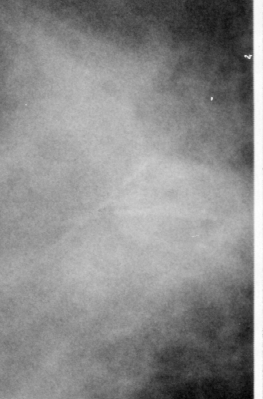
Crop from a digitized film mammogram around one marked abnormality; right breast; CC view; BI-RADS breast density category 3 (scale 1–4).
- Marked abnormality: mass, shape irregular, margins obscured / ill defined; BI-RADS assessment category 4; subtlety rating 3 on a 1 (subtle) to 5 (obvious) scale; pathology result (as recorded, not read from the image): benign.